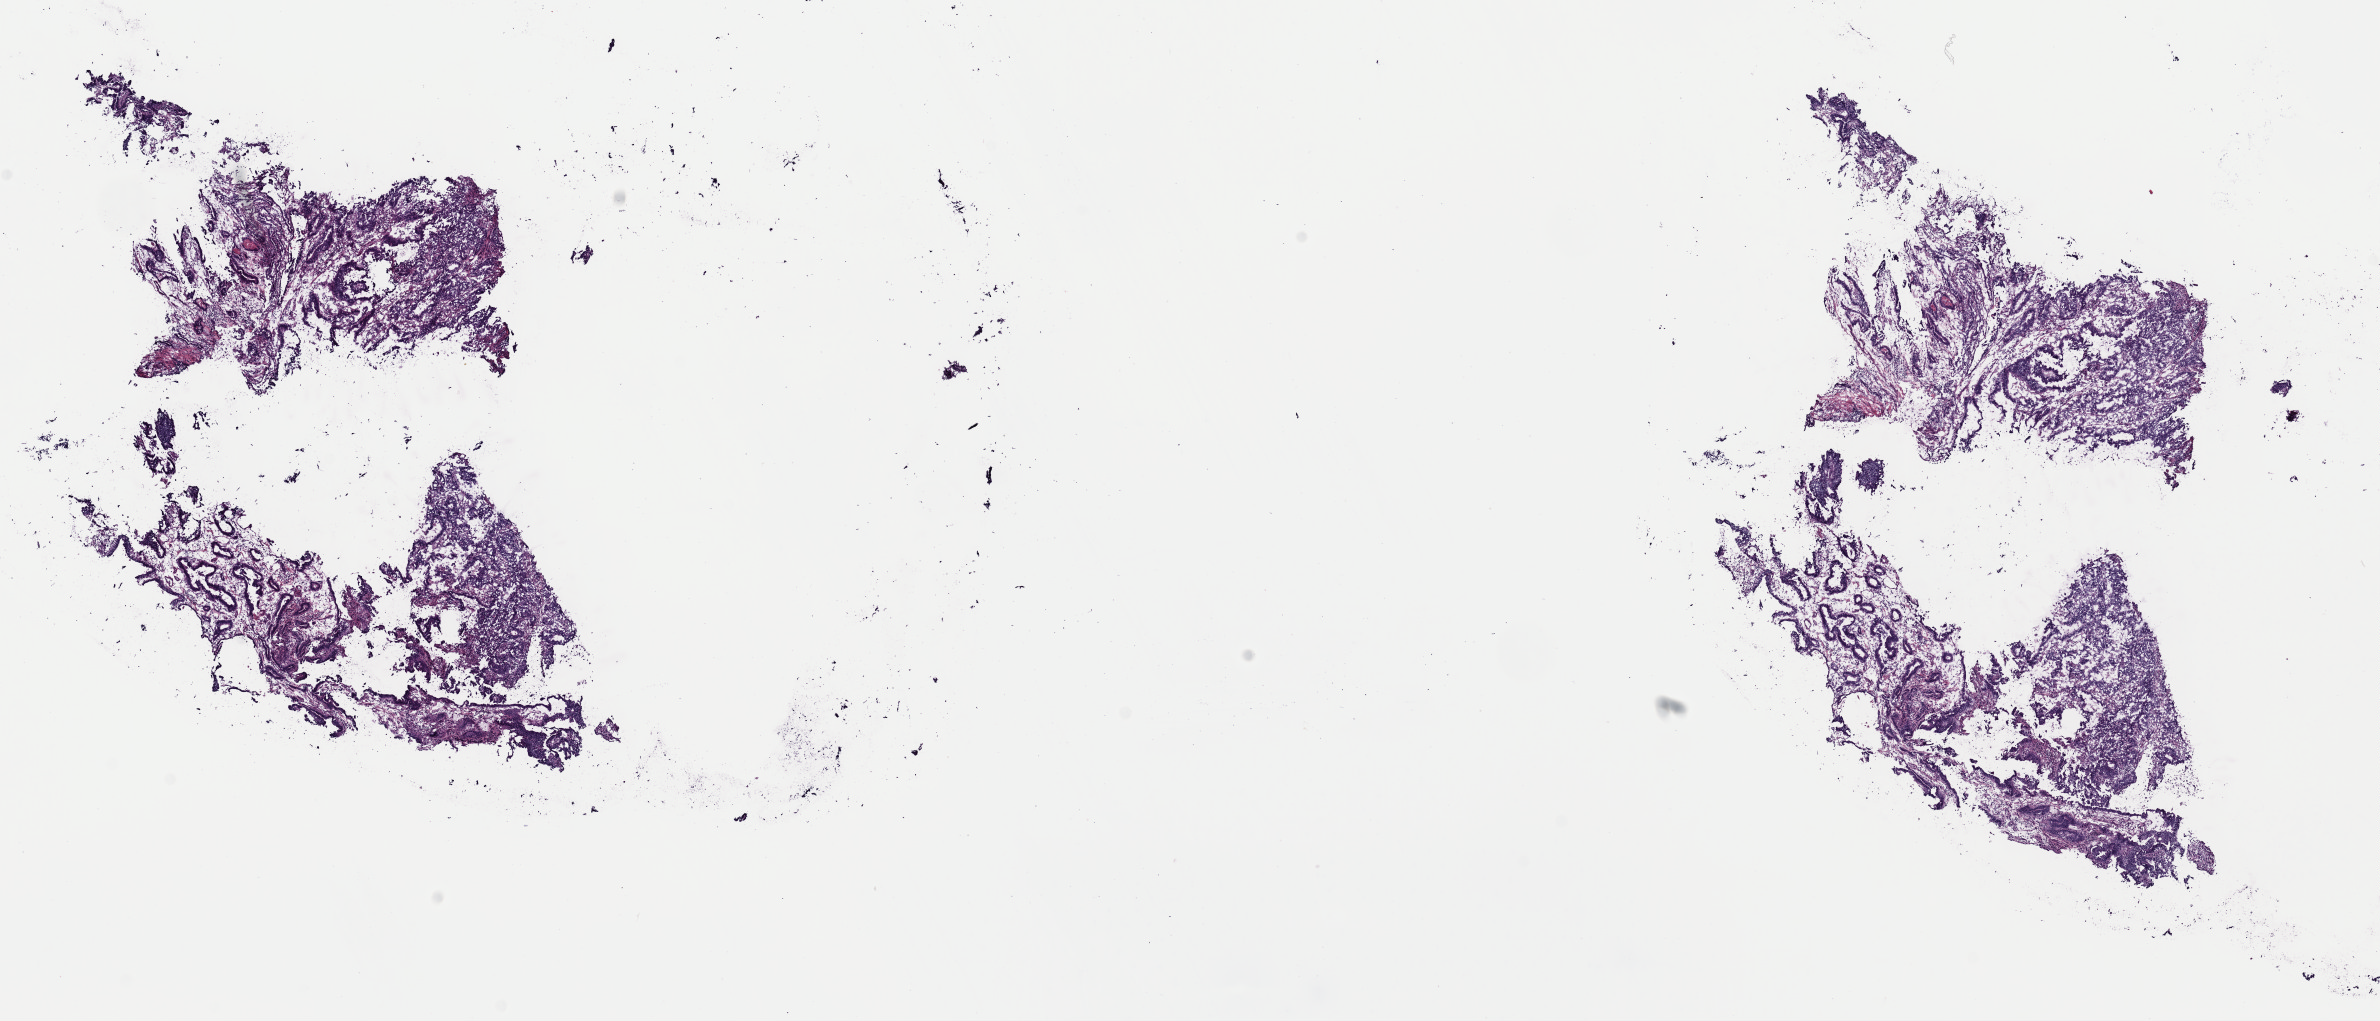
Whole-slide histology image, H&E-stained, a low-resolution overview of the entire scanned area, about 18.8 x 8.1 mm (acquisition: 40x scan), frozen section from the top of the tissue portion, stomach, primary tumour sample. Male patient; age at initial diagnosis 69 years. Histologic grade: G2 (moderately differentiated). Composition of this section per pathologist review: tumour cells 100%, tumour nuclei 75%, normal cells 0%, stromal cells 0%, necrosis 0%. Infiltration values recorded for this section: lymphocyte infiltration 3%, monocyte infiltration 1%, neutrophil infiltration 1%.
AJCC pathologic stage: IIA (7th edition). Histologic diagnosis: Tubular adenocarcinoma (gastric antrum).